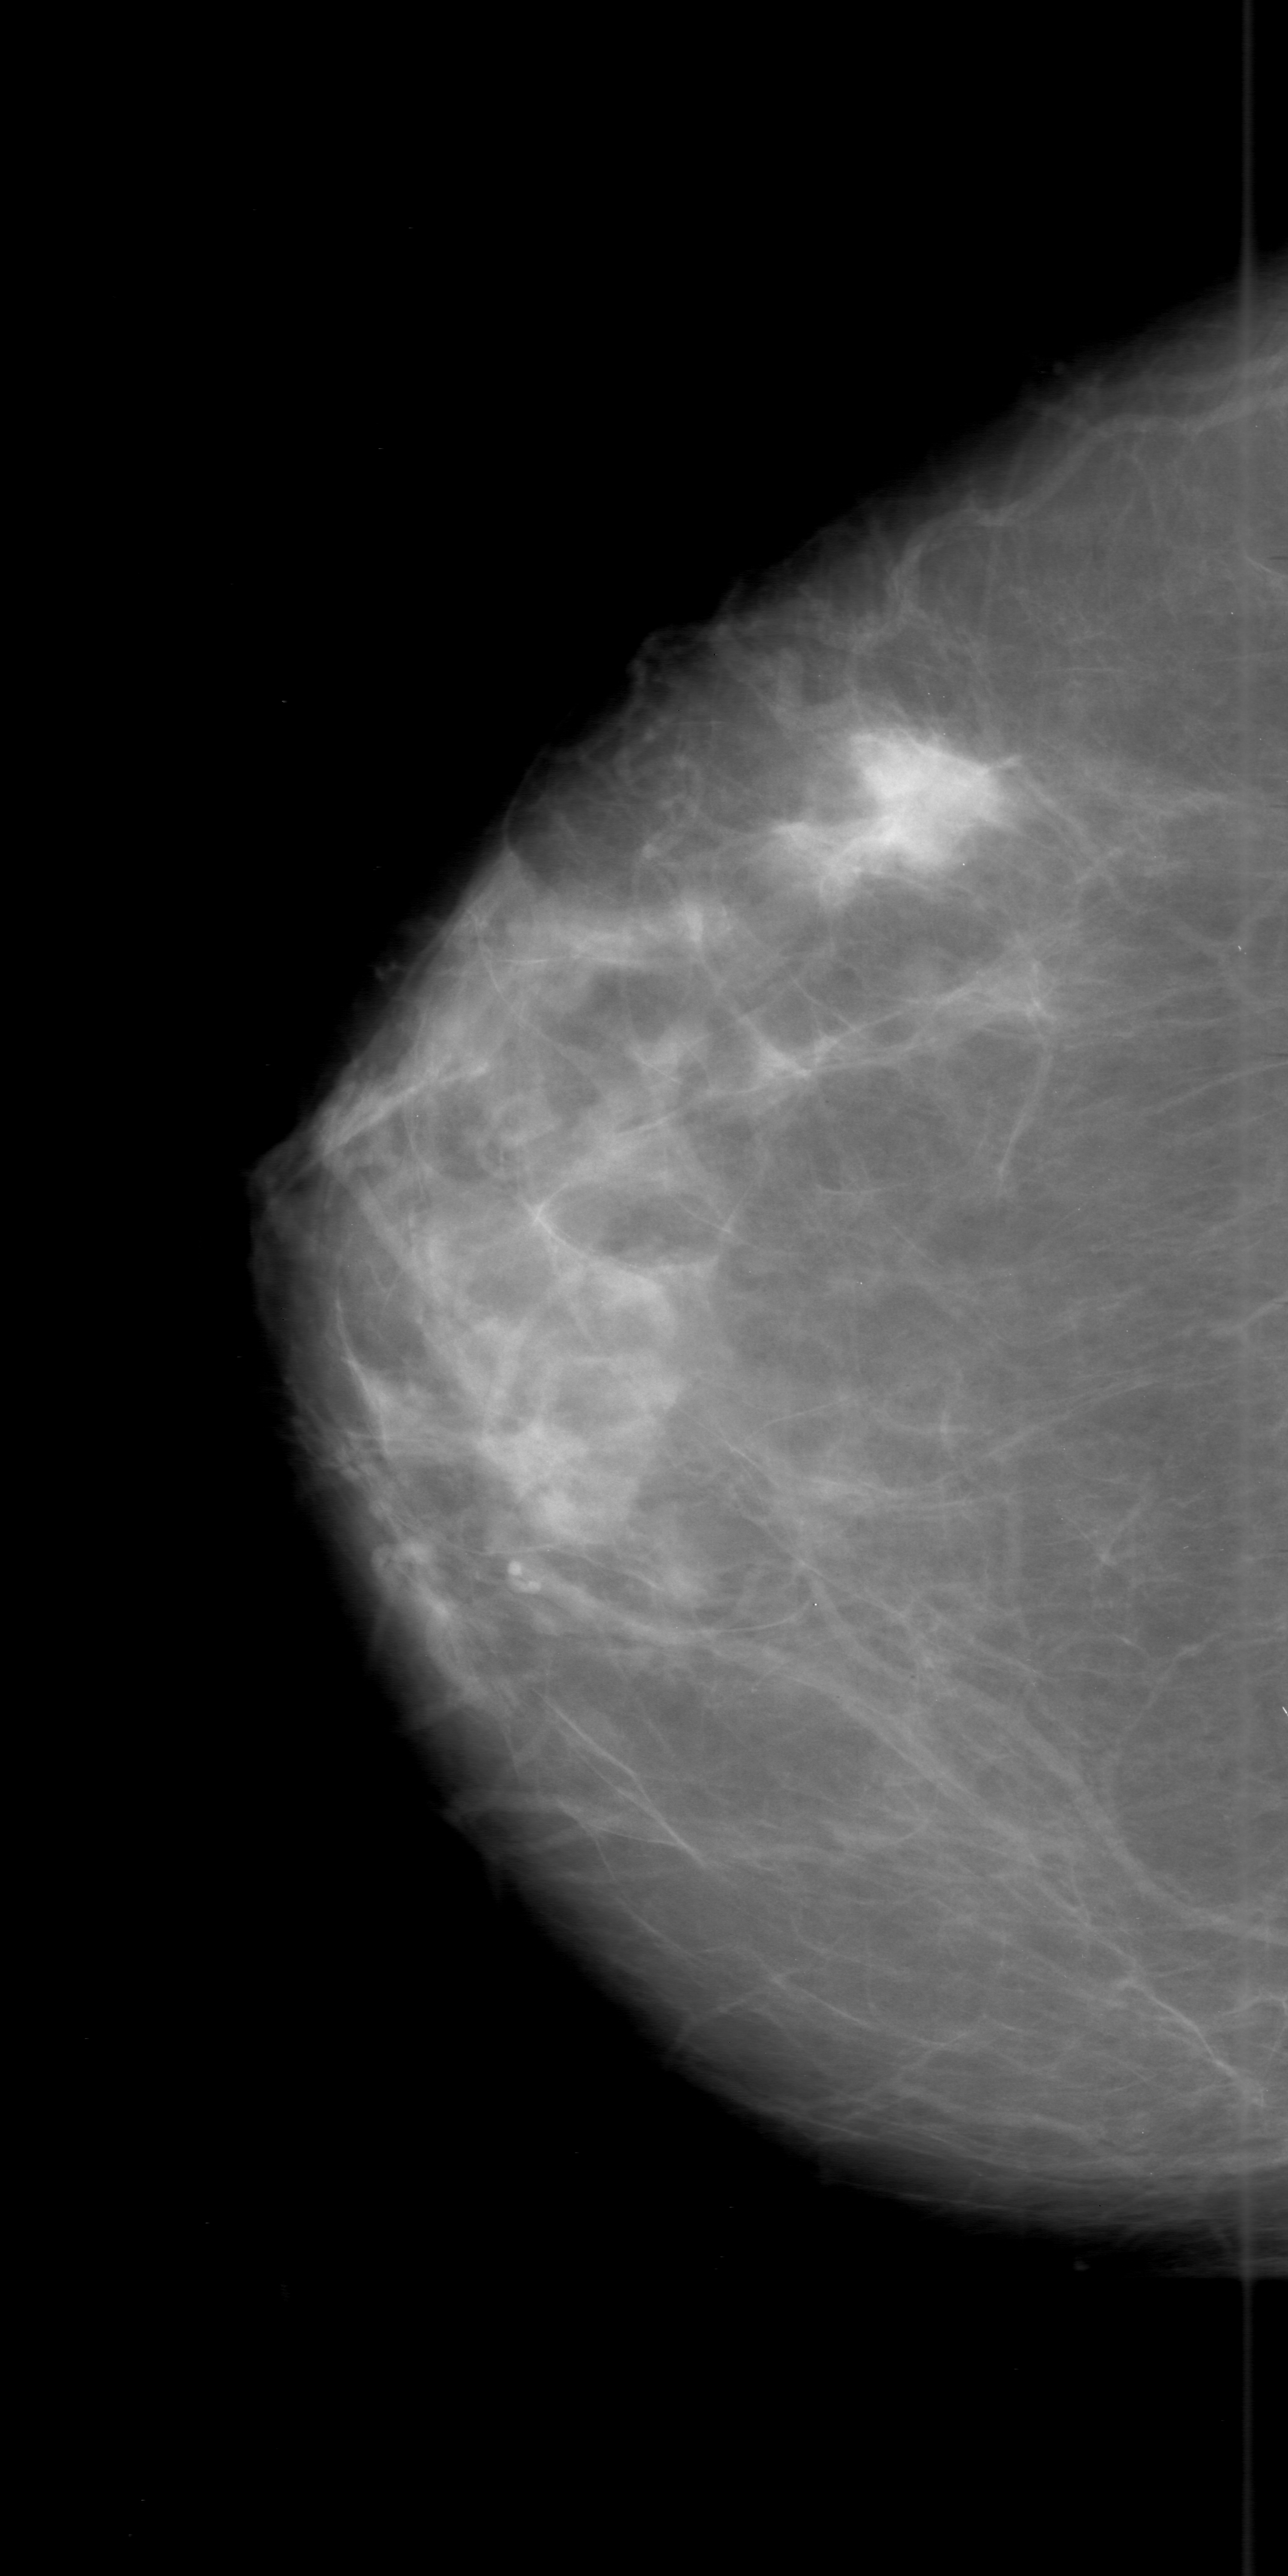
Mammogram (digitized film), right breast, CC view, BI-RADS breast density category 2 (scale 1–4).
Marked abnormality: mass, shape irregular, margins ill defined; BI-RADS assessment category 3; subtlety rating 5 on a 1 (subtle) to 5 (obvious) scale; pathology result (as recorded, not read from the image): malignant.